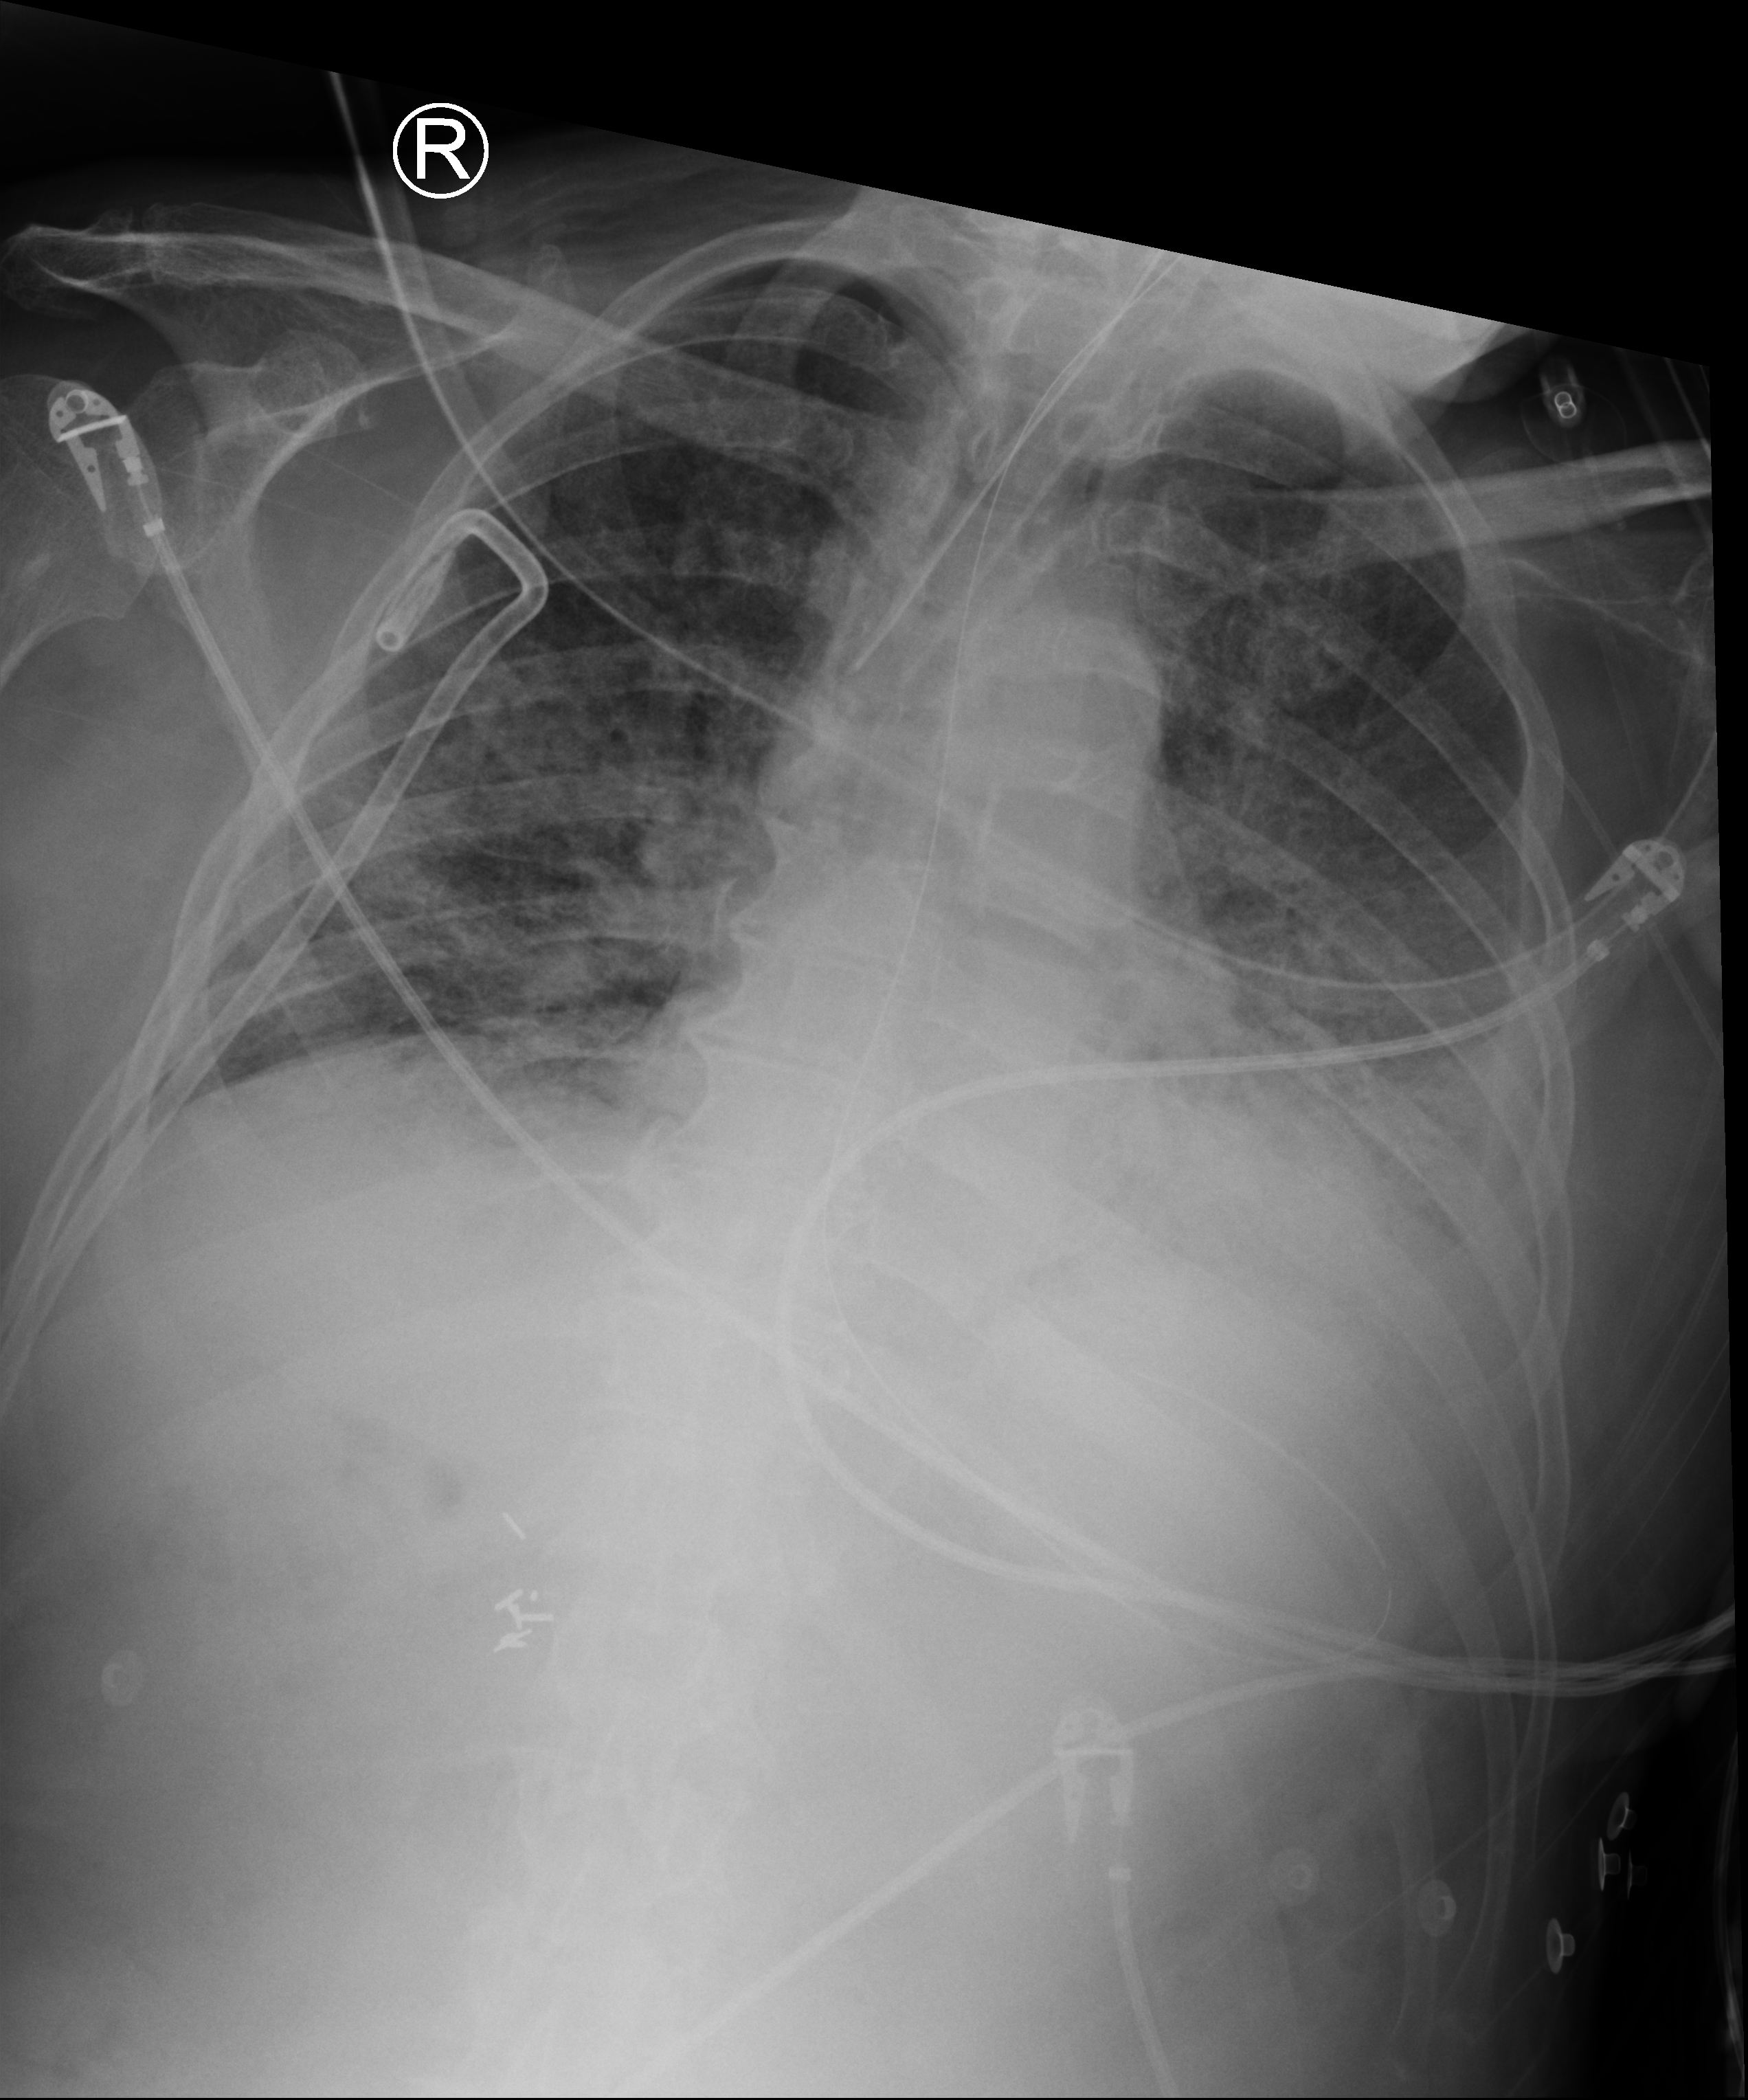
Bedside chest radiograph (computed radiography), anteroposterior (AP) projection. Male patient hospitalised with COVID-19, age 75–90 years.
Hospital-stay facts (about this admission, not read from this image; timing relative to this image not recorded): COPD (admission record): no; mechanically ventilated during this hospital stay: yes.